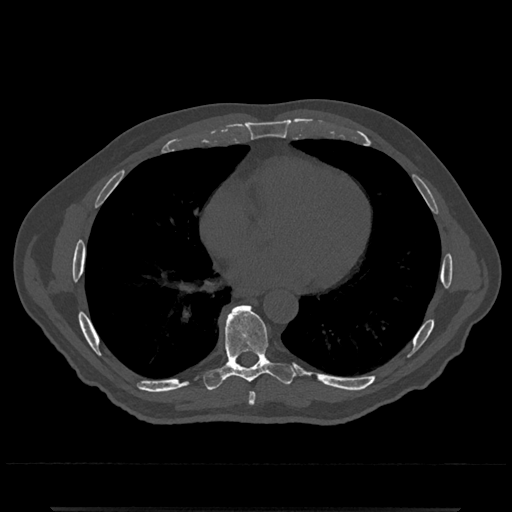
CT including the spine, one axial slice. Position 671 of 797 along the scan axis. Reconstruction kernel Br40s/3. 120 kVp. Bone window (W 1800 / L 400 HU). 512 × 512 image matrix, field of view 393 × 393 mm. Patient: male, 67 years. Case-level facts recorded for this patient, not image findings: primary cancer: prostate.
Outlined on this slice (semi-automatically segmented with operator editing):
- T7 vertebra: bounding box <248,391,256,406> (left, top, right, bottom; pixels)
- T8 vertebra: <203,305,295,390>